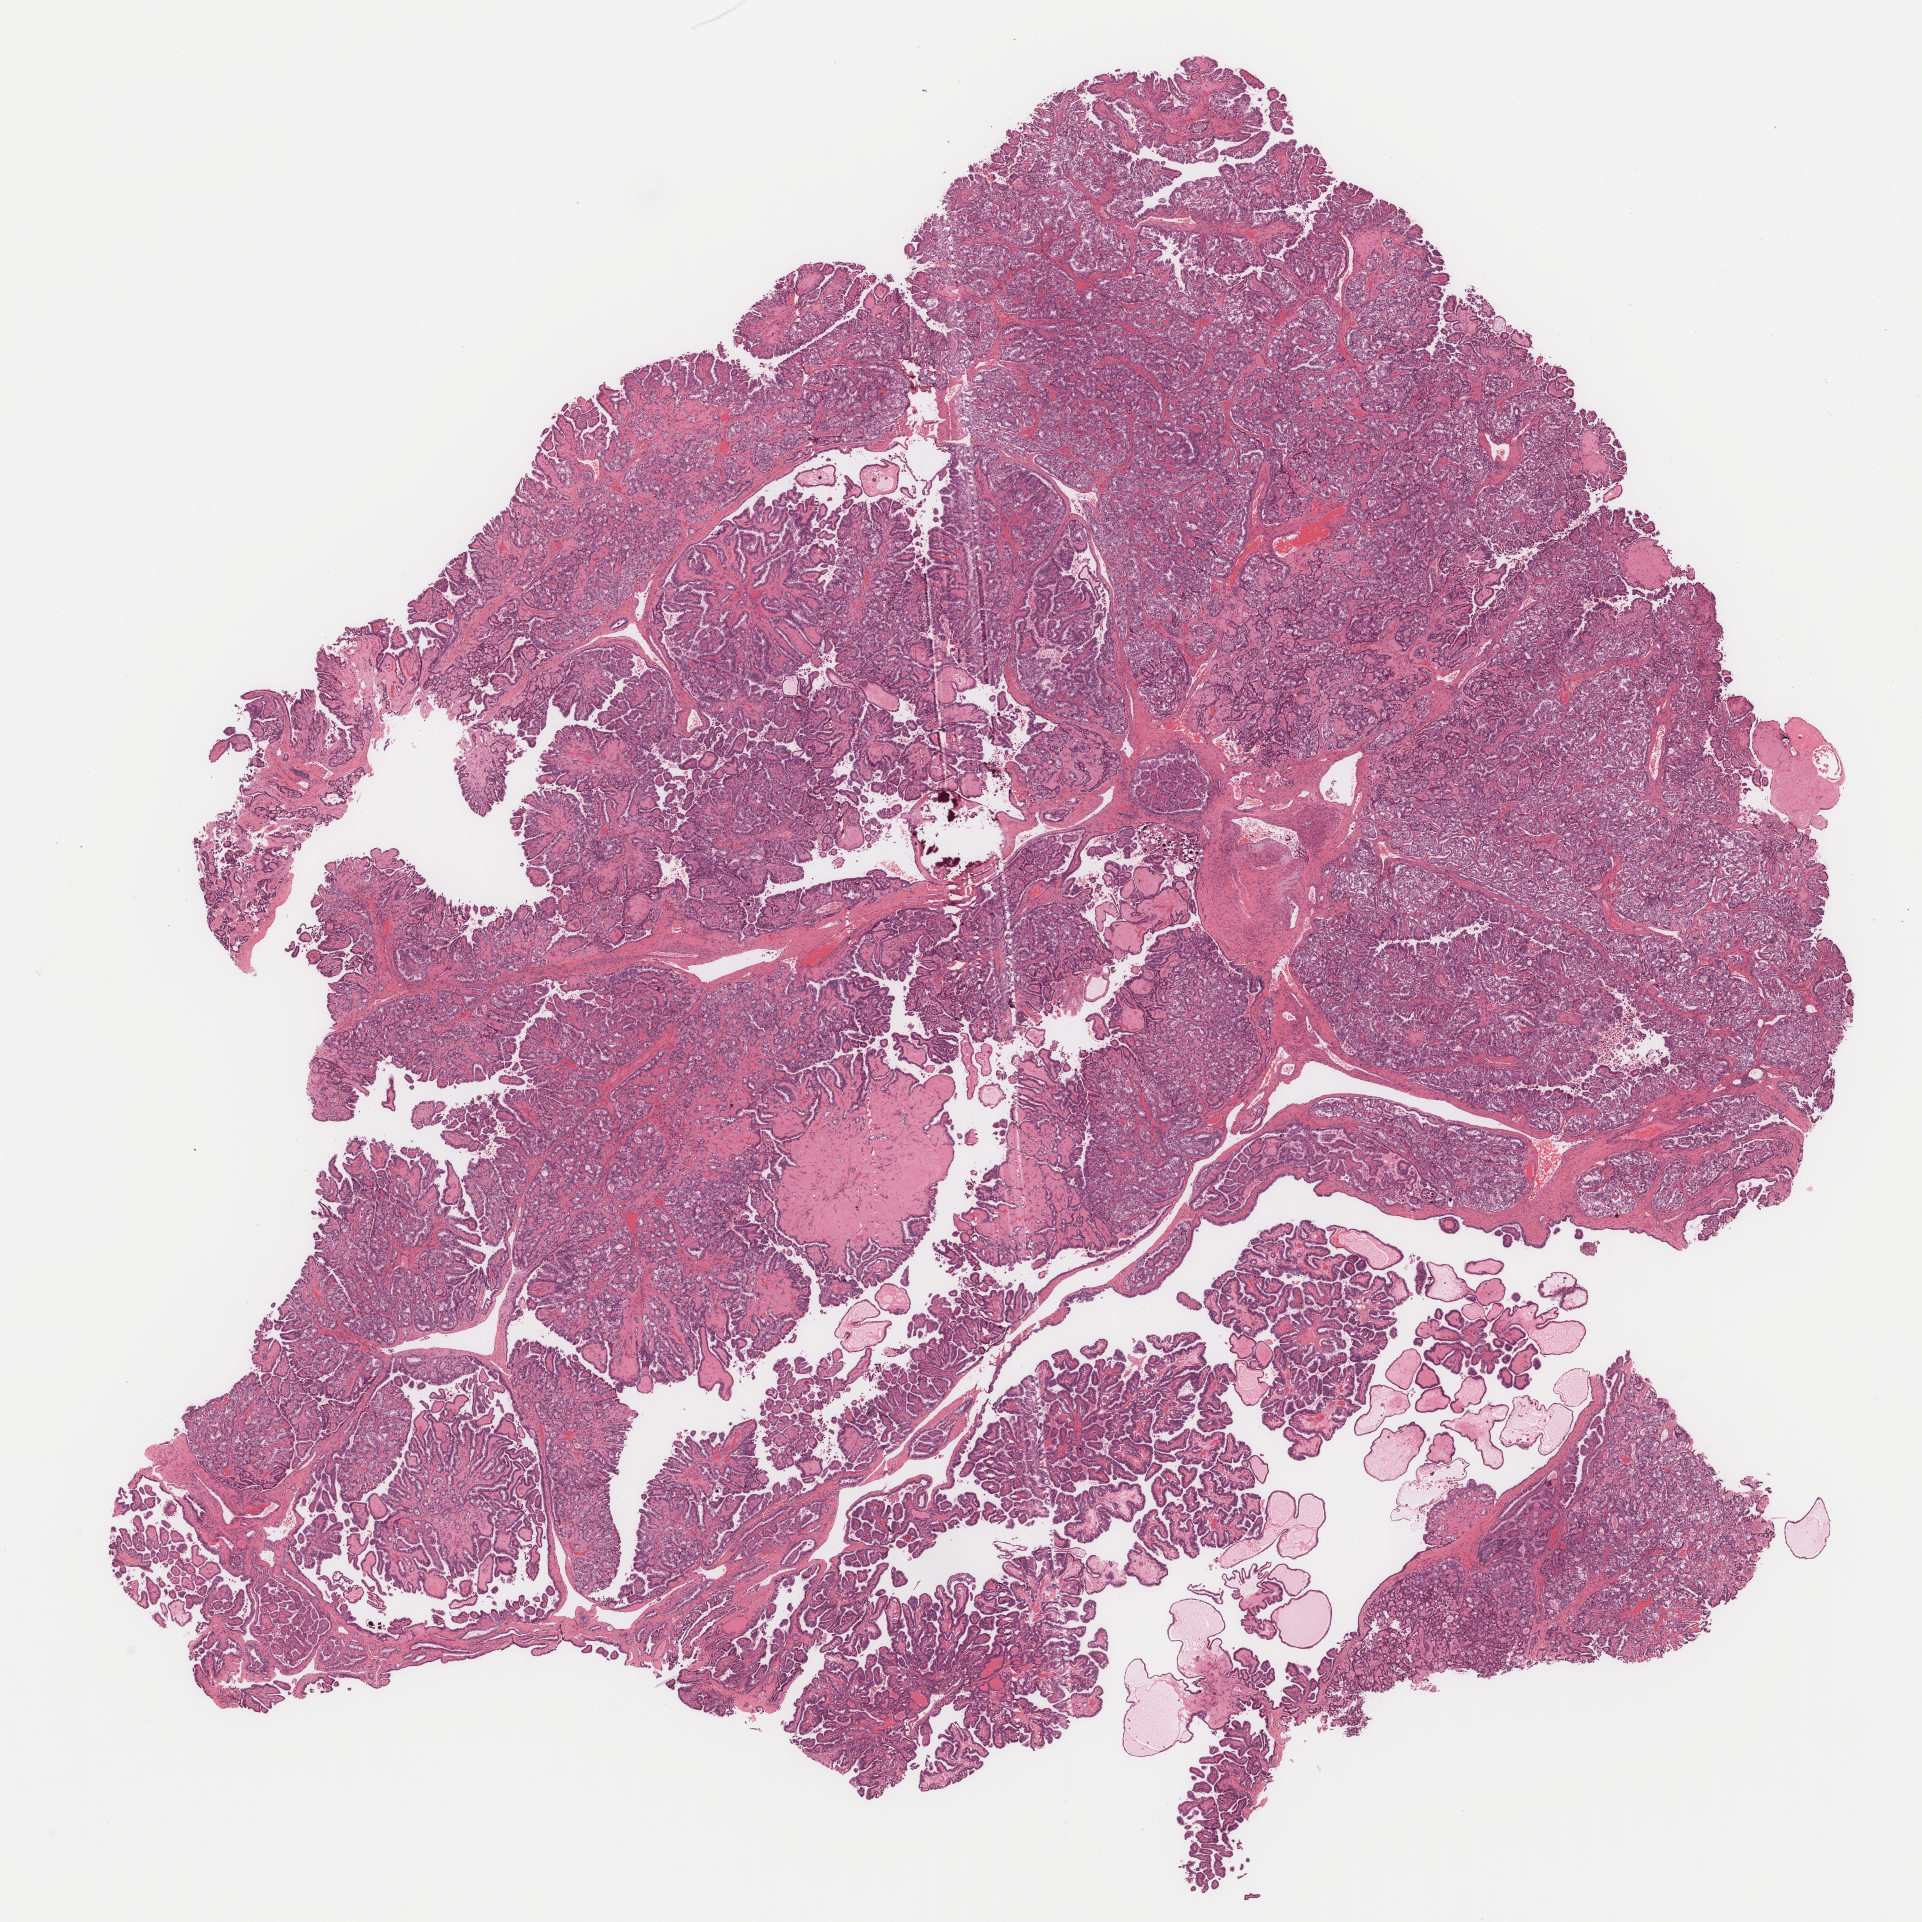
Hematoxylin and eosin (H&E) stained whole-slide image — low-resolution overview of the scanned area, about 15.5 x 15.5 mm (slide scanned at 40x). FFPE section. Sample: primary tumour, thyroid. Patient: male, age at initial diagnosis 40 years.
Lymph nodes positive (case pathology): 0 of 3 examined. Laterality: midline. Histologic diagnosis: Papillary adenocarcinoma, NOS (thyroid gland). AJCC pathologic stage: I (7th edition).